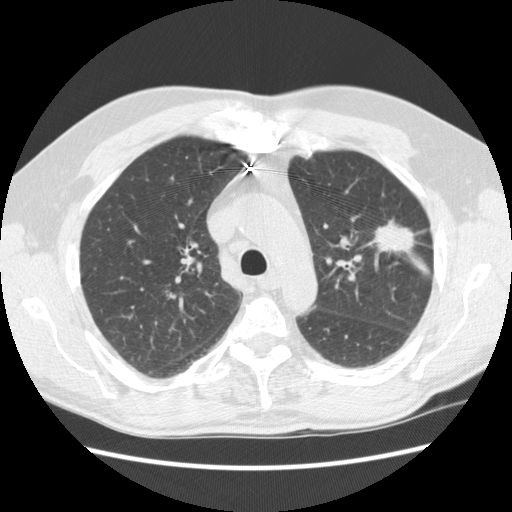
Chest CT (low-dose screening protocol), one axial image, baseline screening round, lung window (W 1500 / L -600 HU), 2.5 mm slice thickness, standard (soft-tissue) reconstruction kernel (STANDARD), 120 kVp. Male participant, aged 72 years at enrolment. Former smoker at enrolment.
- Expert-annotated lung lesion, box from (x=356, y=207) to (x=428, y=259) px.
- Screening reader's record for this exam (one nodule recorded; not confirmed to be the boxed lesion): non-calcified nodule or mass ≥4 mm, left upper lobe, 25 × 18 mm, spiculated (stellate) margins, soft tissue attenuation.
- Later outcome: lung cancer diagnosed 35 days after this screen — adenocarcinoma, NOS, left upper lobe, well differentiated (G1), stage IIIB (AJCC 6th edition), 25 mm at pathology.